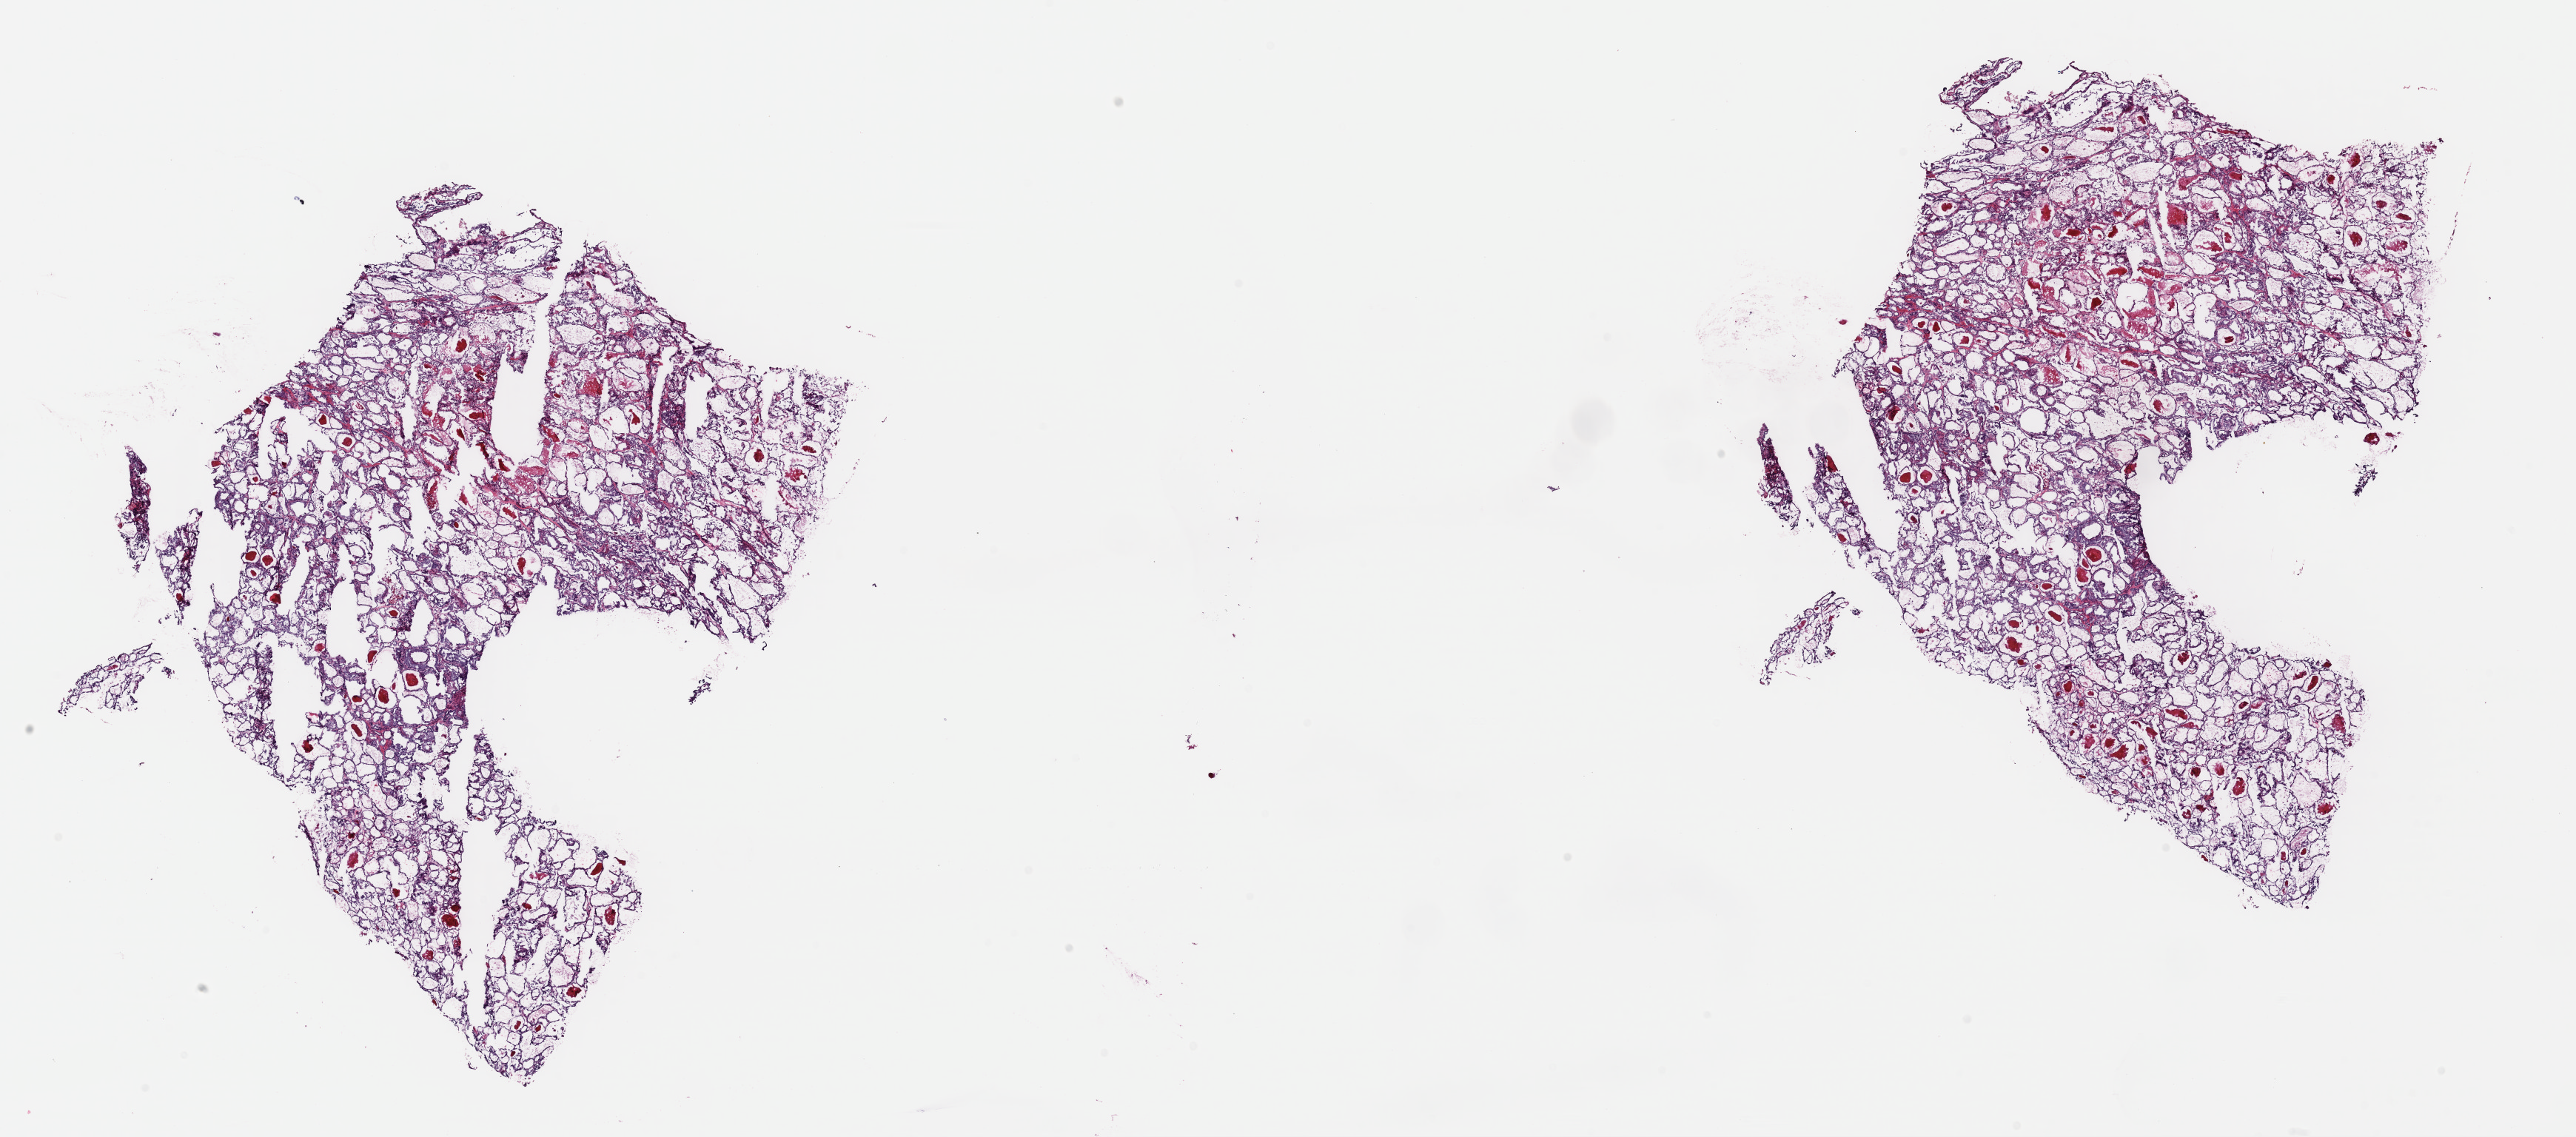
Digitized Hematoxylin and eosin (H&E) stained tissue section (whole slide), low-resolution overview of the scanned area, about 27.5 x 12.1 mm (acquisition: 40x scan), frozen section, thyroid, primary tumour sample. Female, age 53 years at initial diagnosis. Slide review estimates, as recorded: tumour cells 60%, tumour nuclei 100%, normal cells 0%, stromal cells 40%, necrosis 0%. Inflammatory infiltration, as recorded: lymphocyte infiltration 0%, monocyte infiltration 1%, neutrophil infiltration 0%.
• lymph nodes positive (case pathology): 0 of 7 examined
• histologic diagnosis: Papillary adenocarcinoma, NOS (thyroid gland)
• AJCC pathologic stage: II (7th edition)